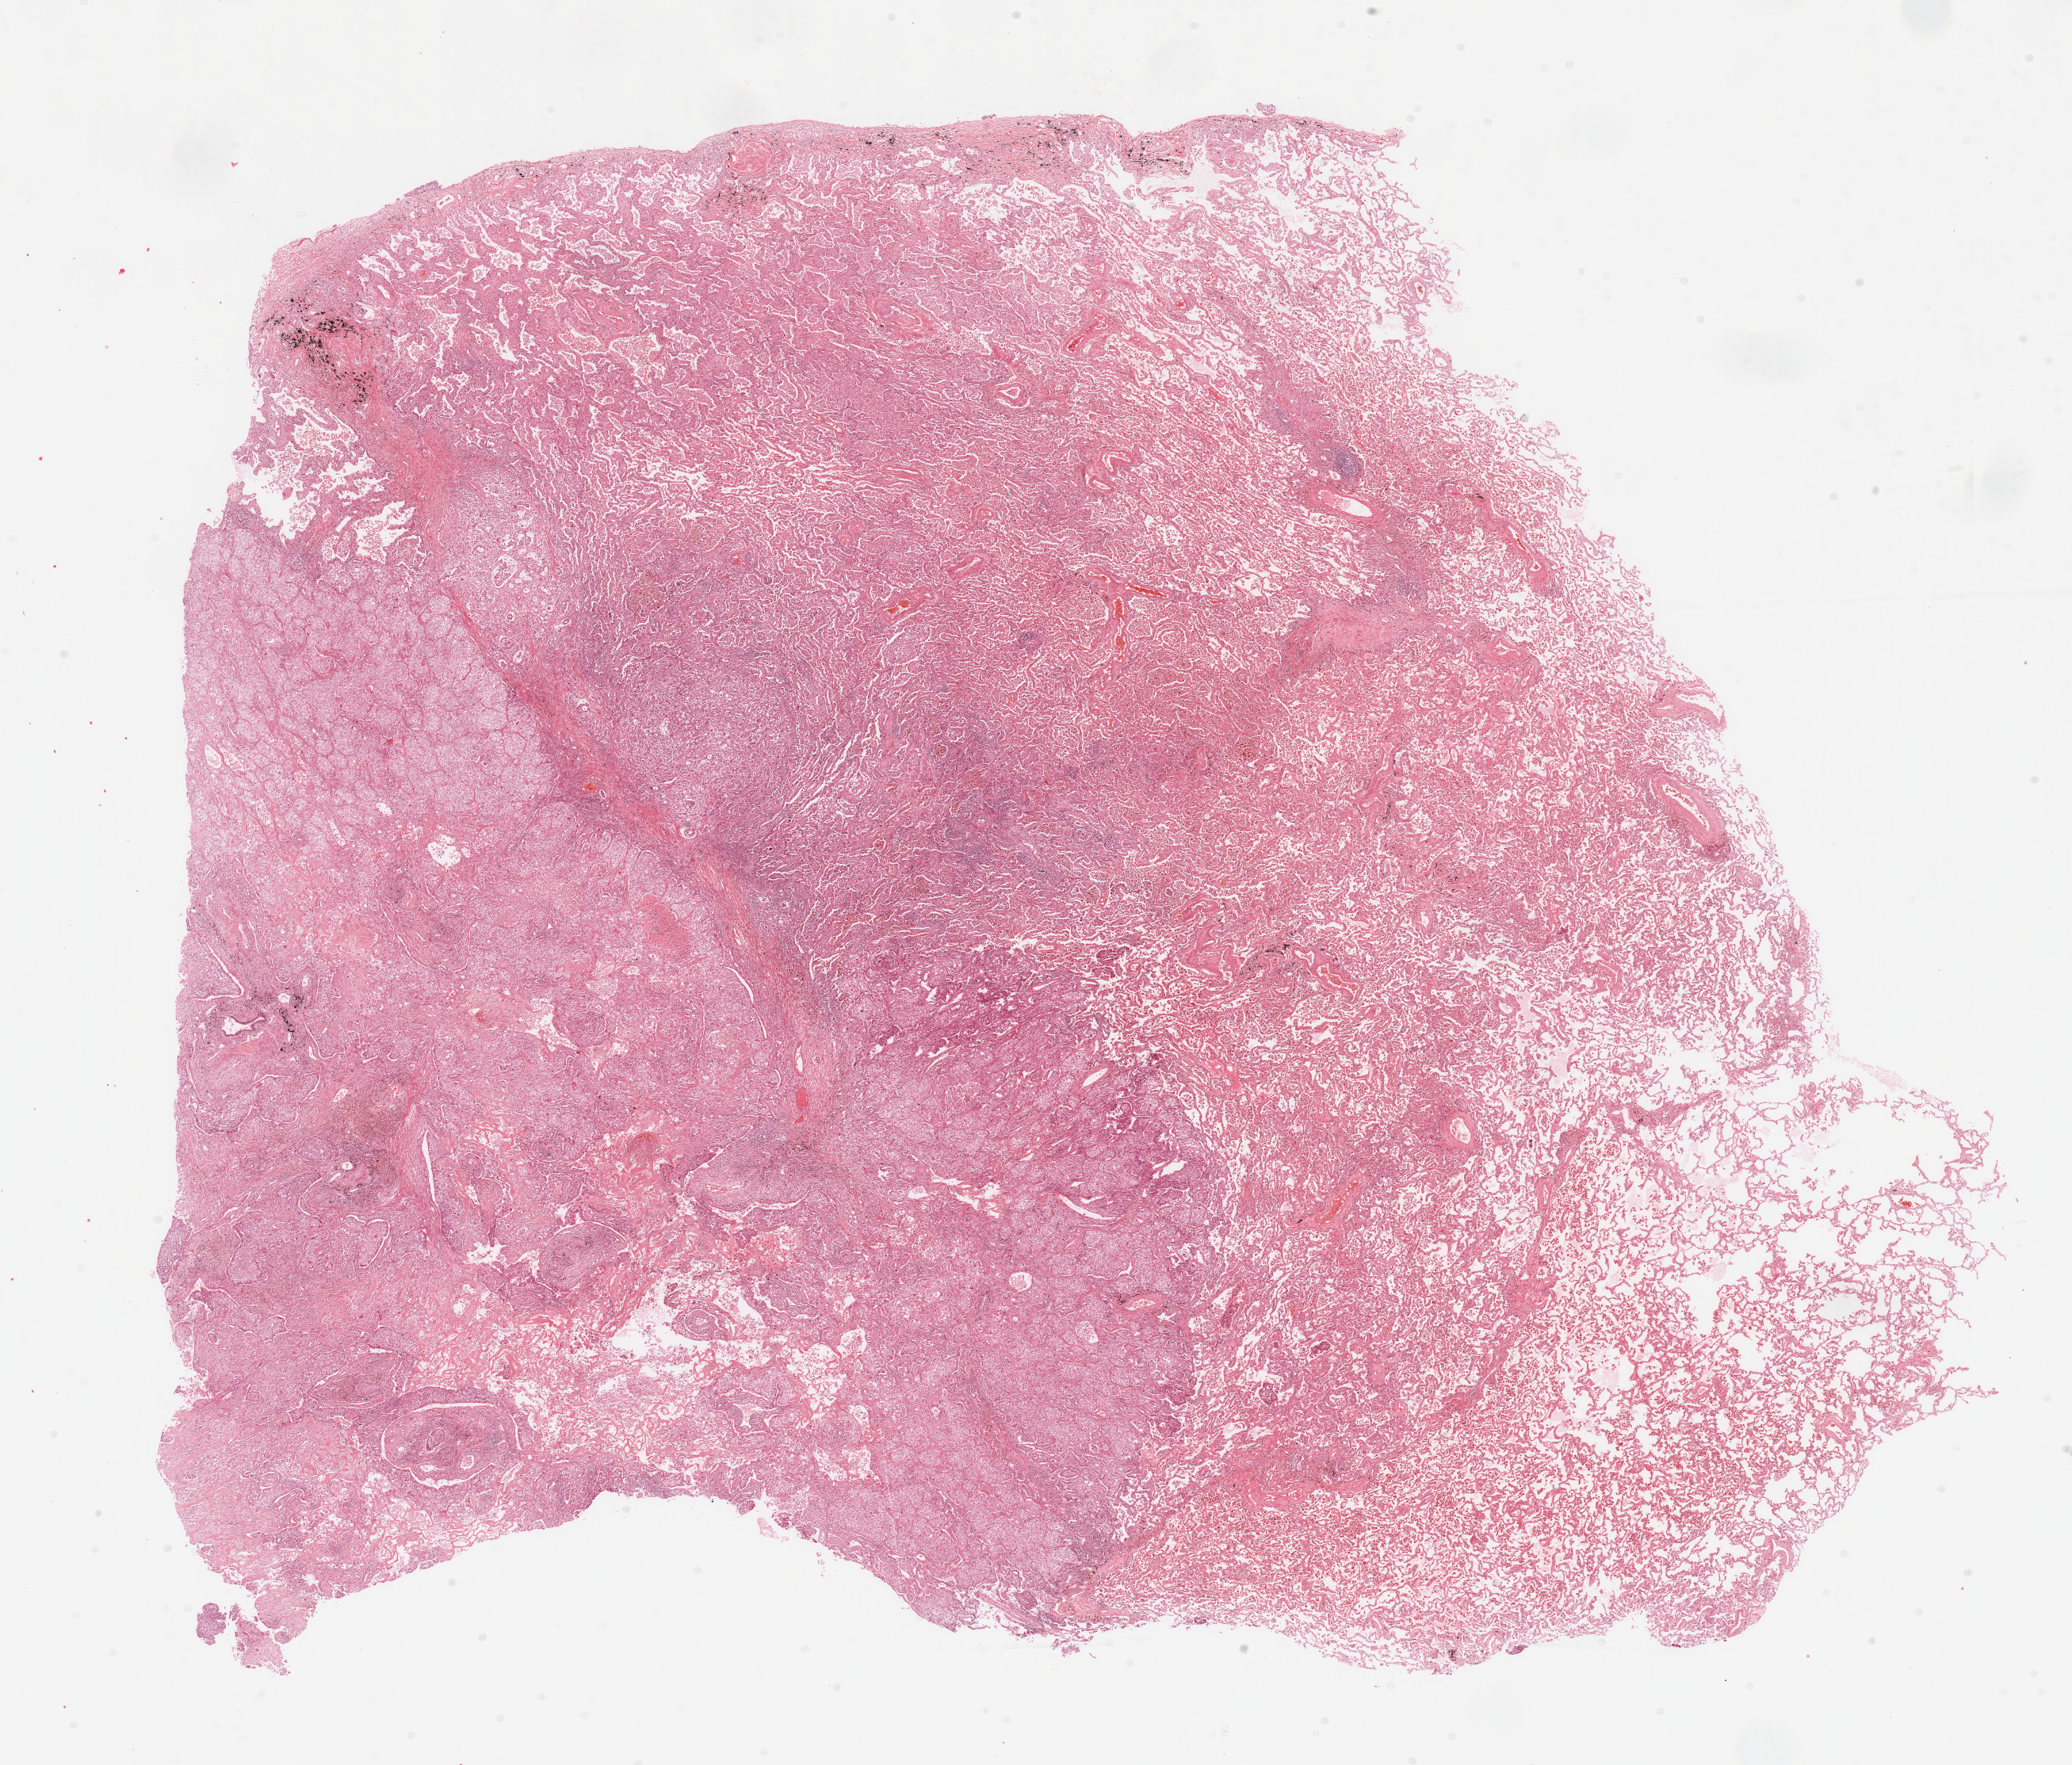
Digitized H&E tissue section (whole slide) — a low-resolution overview of the entire scanned area, about 20.7 x 17.6 mm (from a 20x scan); tumour tissue sample, lung. Male, 57 y/o. Histologic grade: G2 (moderately differentiated).
Histologic diagnosis: Adenocarcinoma, NOS. AJCC pathologic stage: IB.